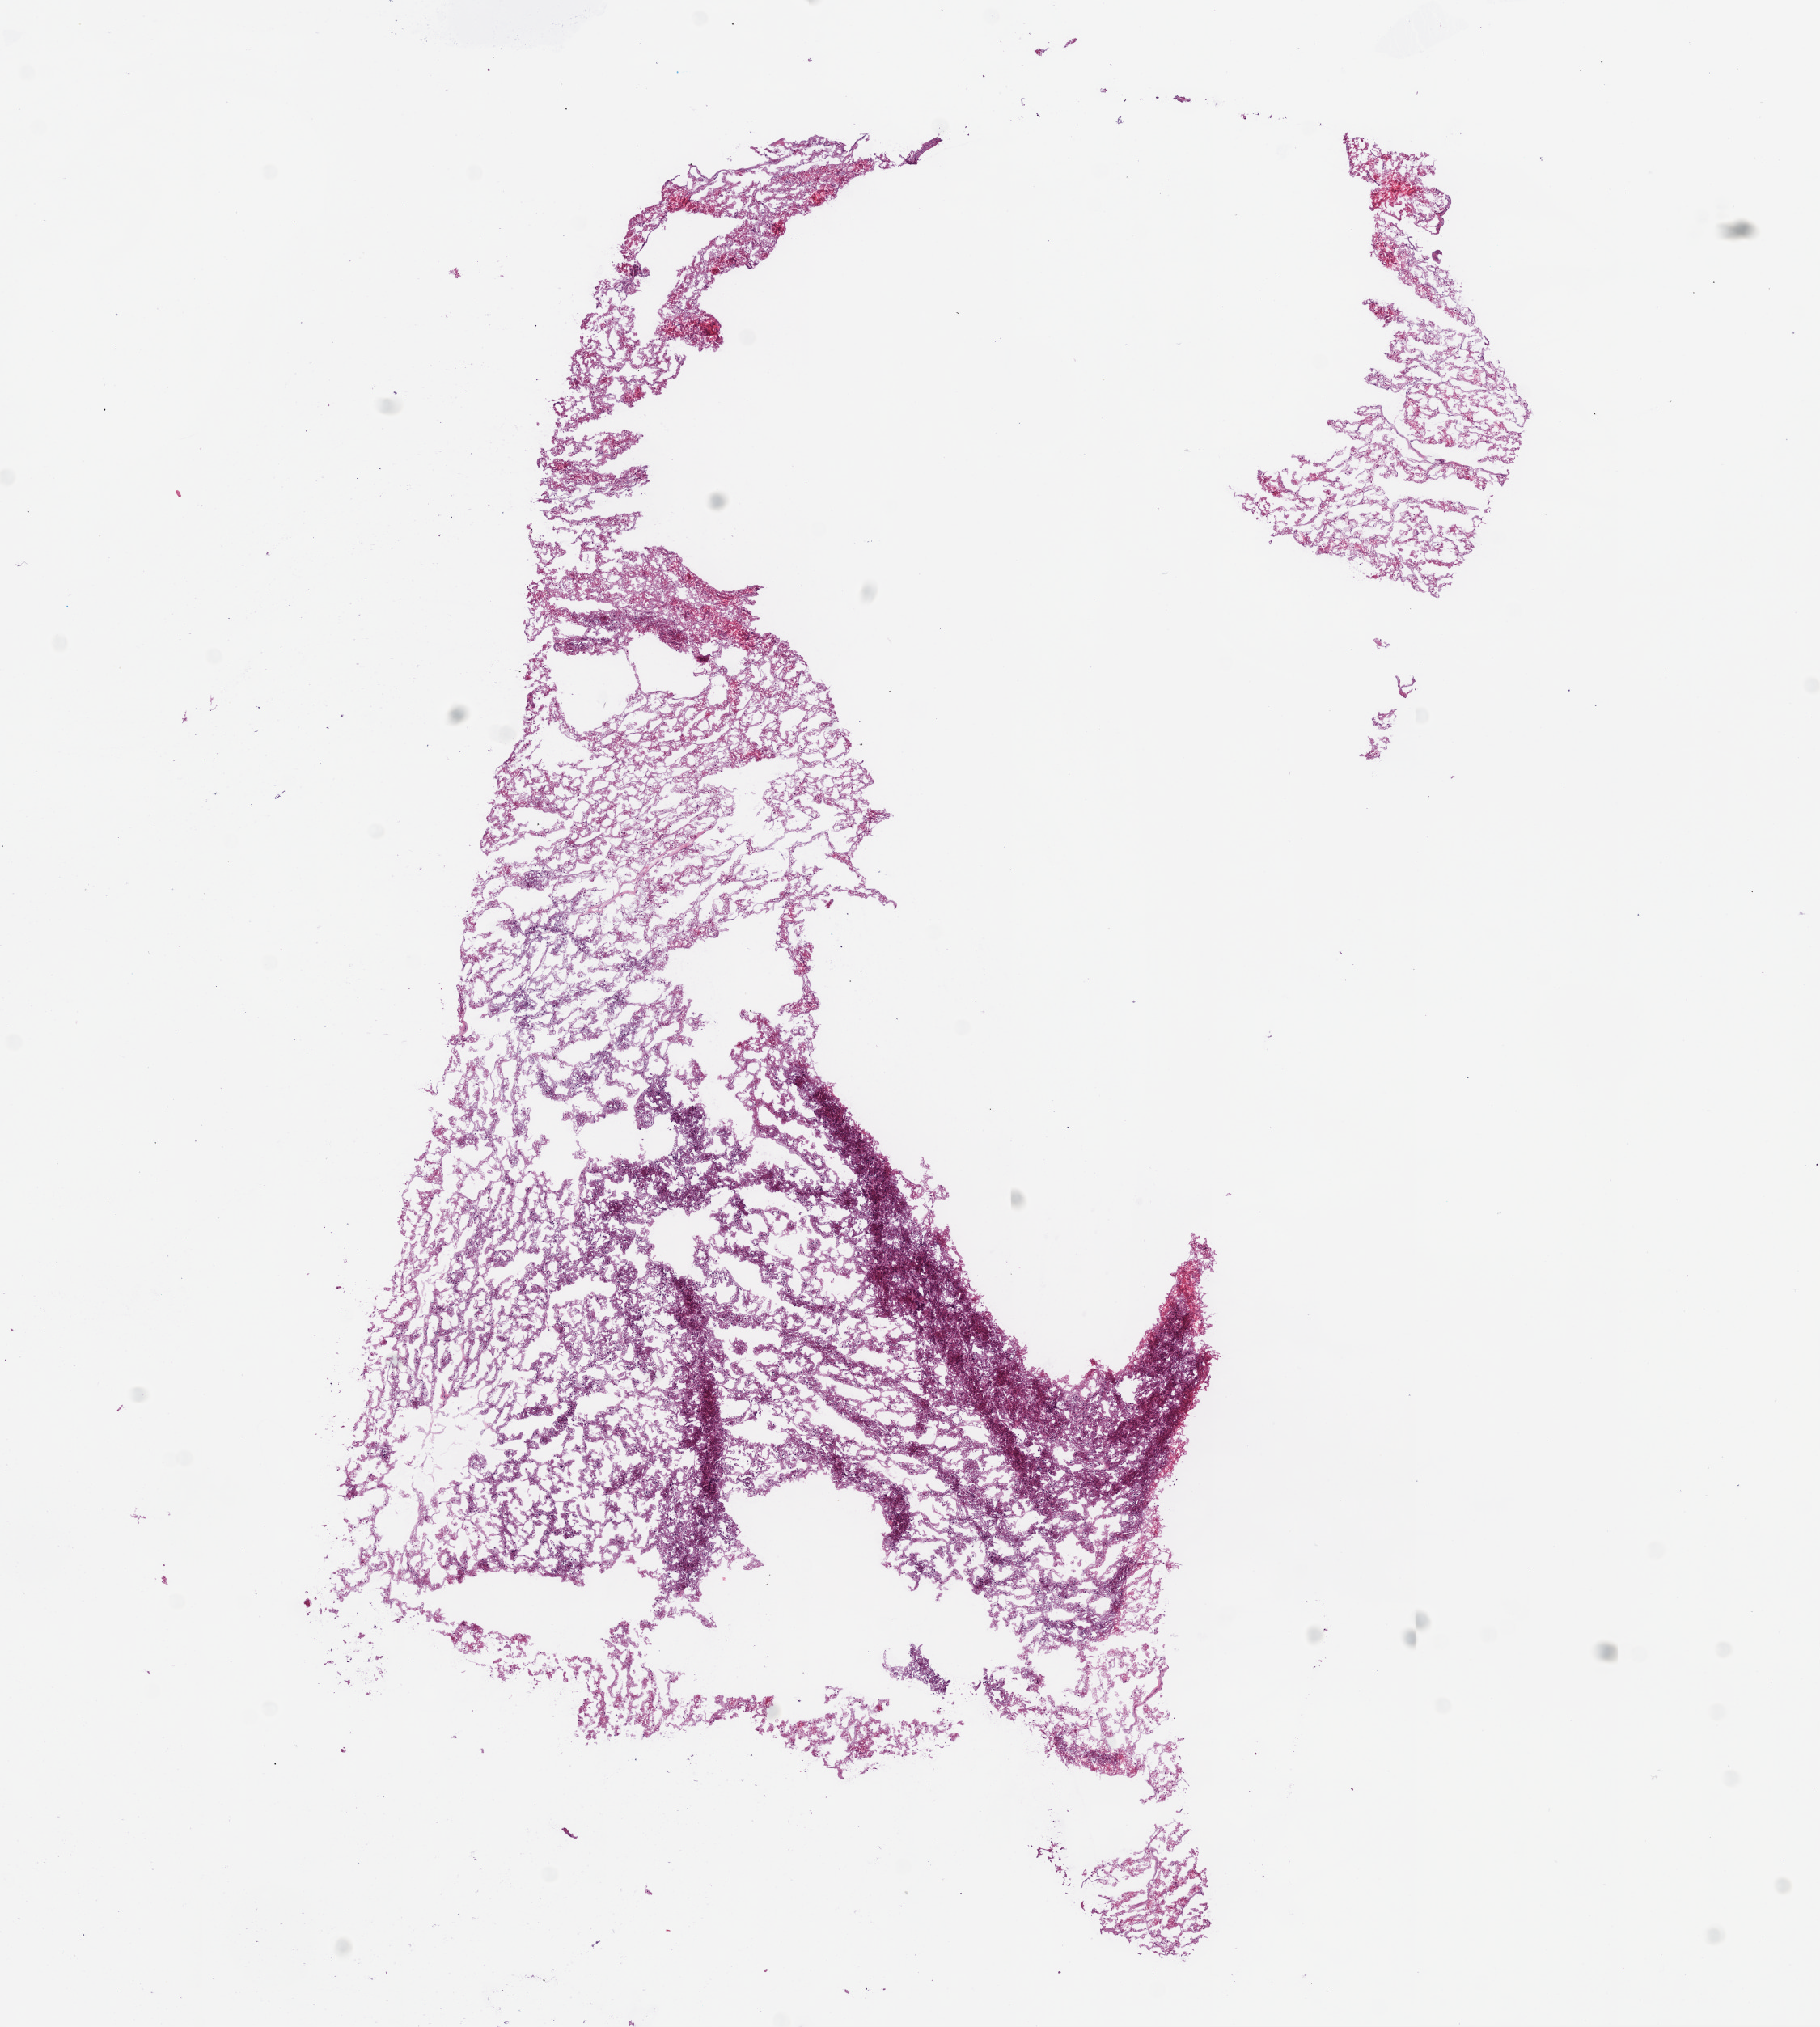
H&E whole-slide image, whole scanned area (about 9.0 x 10.1 mm) shown as a low-resolution overview; frozen section; sample: primary tumour, kidney. Patient: male, age at initial diagnosis 83 years. Histologic grade: G2 (moderately differentiated). Composition of this section per pathologist review: tumour cells 93%, tumour nuclei 85%, normal cells 0%, stromal cells 5%, necrosis 2%.
Pathologic diagnosis: Clear cell adenocarcinoma, NOS. TNM: T2 NX M0. Laterality: left. AJCC pathologic stage: II.